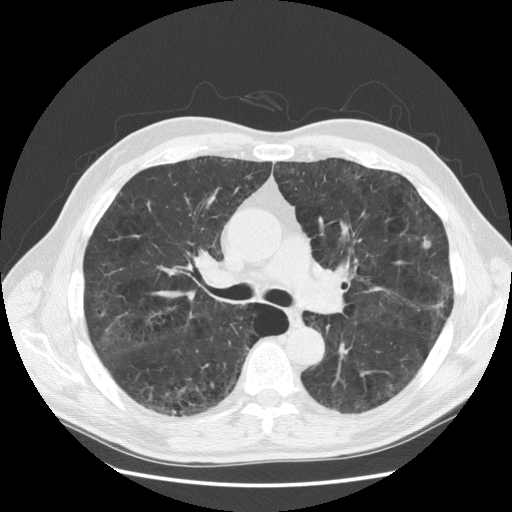
Low-dose screening chest CT, one axial slice; slice 94 of 163 in the series (ordered by position); lung window (W 1500 / L -600 HU); 512 × 512 image matrix.
Outlined on this slice (expert manual segmentation):
- lesion 1 (tumor, upper lobe of left lung): box from (x=423, y=236) to (x=432, y=248) px